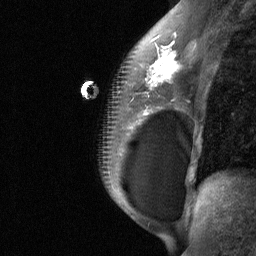
Breast MRI (dynamic contrast-enhanced), one sagittal slice; position 42 of 64 along the scan axis; dynamic contrast-enhanced study with each time point stored as its own series, time point 2 of 3 at this slice position (early post-contrast, ordered by acquisition time); 1.5 T; TE 4.8 ms, TR 27 ms; 256 × 256 image matrix. Patient: female, 34 years. Case-level facts recorded for this patient, not image findings: setting: breast cancer imaged before/during neoadjuvant chemotherapy; receptor status: HR-positive, HER2-negative.
Annotated regions visible in this slice (semi-automatically segmented with operator editing):
- analysis volume of interest (the breast-tissue region the enhancement analysis was run in; not a lesion): bounding box <92,50,188,185> (left, top, right, bottom; pixels)
- tumour enhancement mask (voxels above the 90 % enhancement threshold inside the analysis volume of interest): <144,51,182,114>